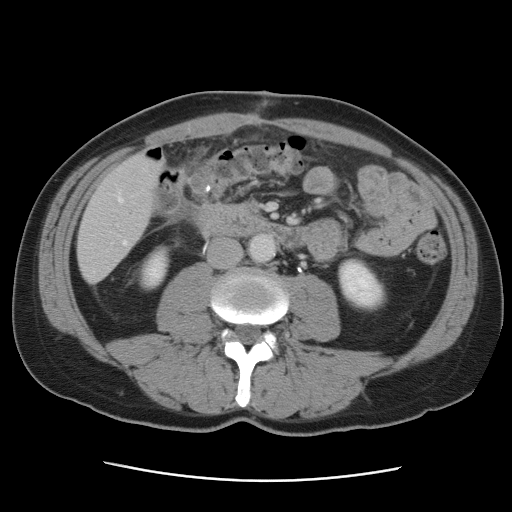
Contrast-enhanced abdominal CT, one axial slice. Slice 18 of 89 in the series (ordered by position). Intravenous contrast given. Soft-tissue window (W 400 / L 40 HU). 5 mm slice thickness. 512 × 512 image matrix, field of view 366 × 366 mm. Male patient, age 59 years. From the clinical record (not read from this slice): diagnosis: colorectal cancer liver metastases, imaged before liver resection; multiple liver metastases: yes; largest metastasis: 0.6 cm; disease in both lobes: yes.
Structures marked on this image (outlined manually by an expert reader):
- hepatic veins: box from (x=117, y=192) to (x=128, y=245) px
- liver: (x=78, y=154)–(x=162, y=282)
- planned liver remnant (the part of the liver to remain after resection): (x=78, y=154)–(x=162, y=256)